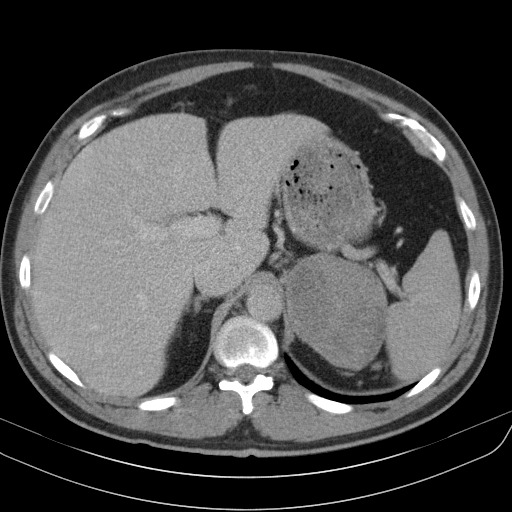
Contrast-enhanced abdominal CT, one axial slice. Position 75 of 91 along the scan axis. Reconstruction kernel B31s. 130 kVp. Intravenous contrast given. Soft-tissue window (W 400 / L 40 HU). 5 mm slice thickness. 512 × 512 image matrix, field of view 370 × 370 mm. Patient: male, 51 years. Case-level facts recorded for this patient, not image findings: diagnosis: adrenocortical carcinoma; tumour side: left adrenal; tumour size at pathology: 18 cm; Ki-67 index: 40 %; stage (as recorded): 3.
Annotated regions visible in this slice (semi-automatic segmentation, software-assisted and operator-edited):
- mass: bounding box [x1, y1, x2, y2] px = [288, 260, 385, 365]